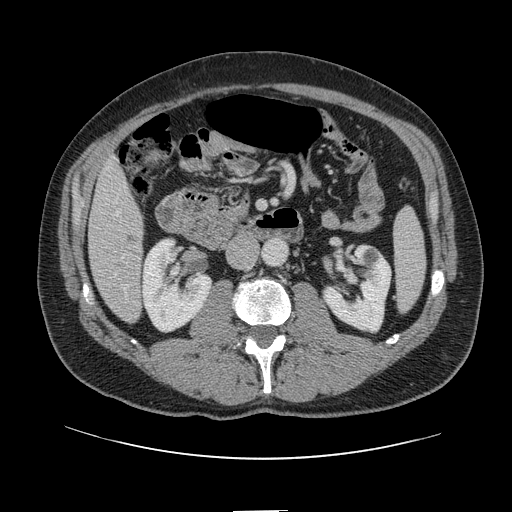
Contrast-enhanced abdominal CT, one axial slice. Slice 32 of 161 in the series (ordered by position). Soft-tissue window (W 400 / L 40 HU). 512 × 512 image matrix, field of view 412 × 412 mm. Male patient, age 66 years. From the clinical record (not read from this slice): diagnosis: colorectal cancer liver metastases, imaged before liver resection.
Outlined on this slice (outlined manually by an expert reader):
- hepatic veins: bounding box (x1, y1, x2, y2) in pixels: (115, 213, 119, 275)
- liver: (89, 161, 144, 322)
- planned liver remnant (the part of the liver to remain after resection): (89, 161, 143, 262)